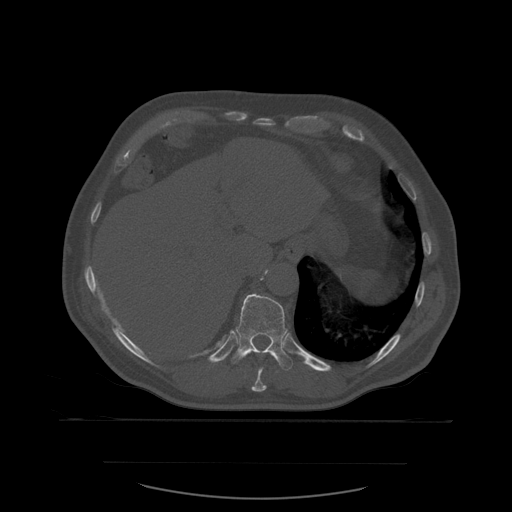
CT including the spine, one axial slice. Position 303 of 590 along the scan axis. Bone window (W 1800 / L 400 HU). 512 × 512 image matrix. Patient age 71 years. Case-level facts recorded for this patient, not image findings: primary cancer: lung.
Annotated regions visible in this slice (semi-automatic segmentation, software-assisted and operator-edited):
- T10 vertebra: box from (x=252, y=368) to (x=267, y=392) px
- T11 vertebra: (x=230, y=294)–(x=294, y=371)